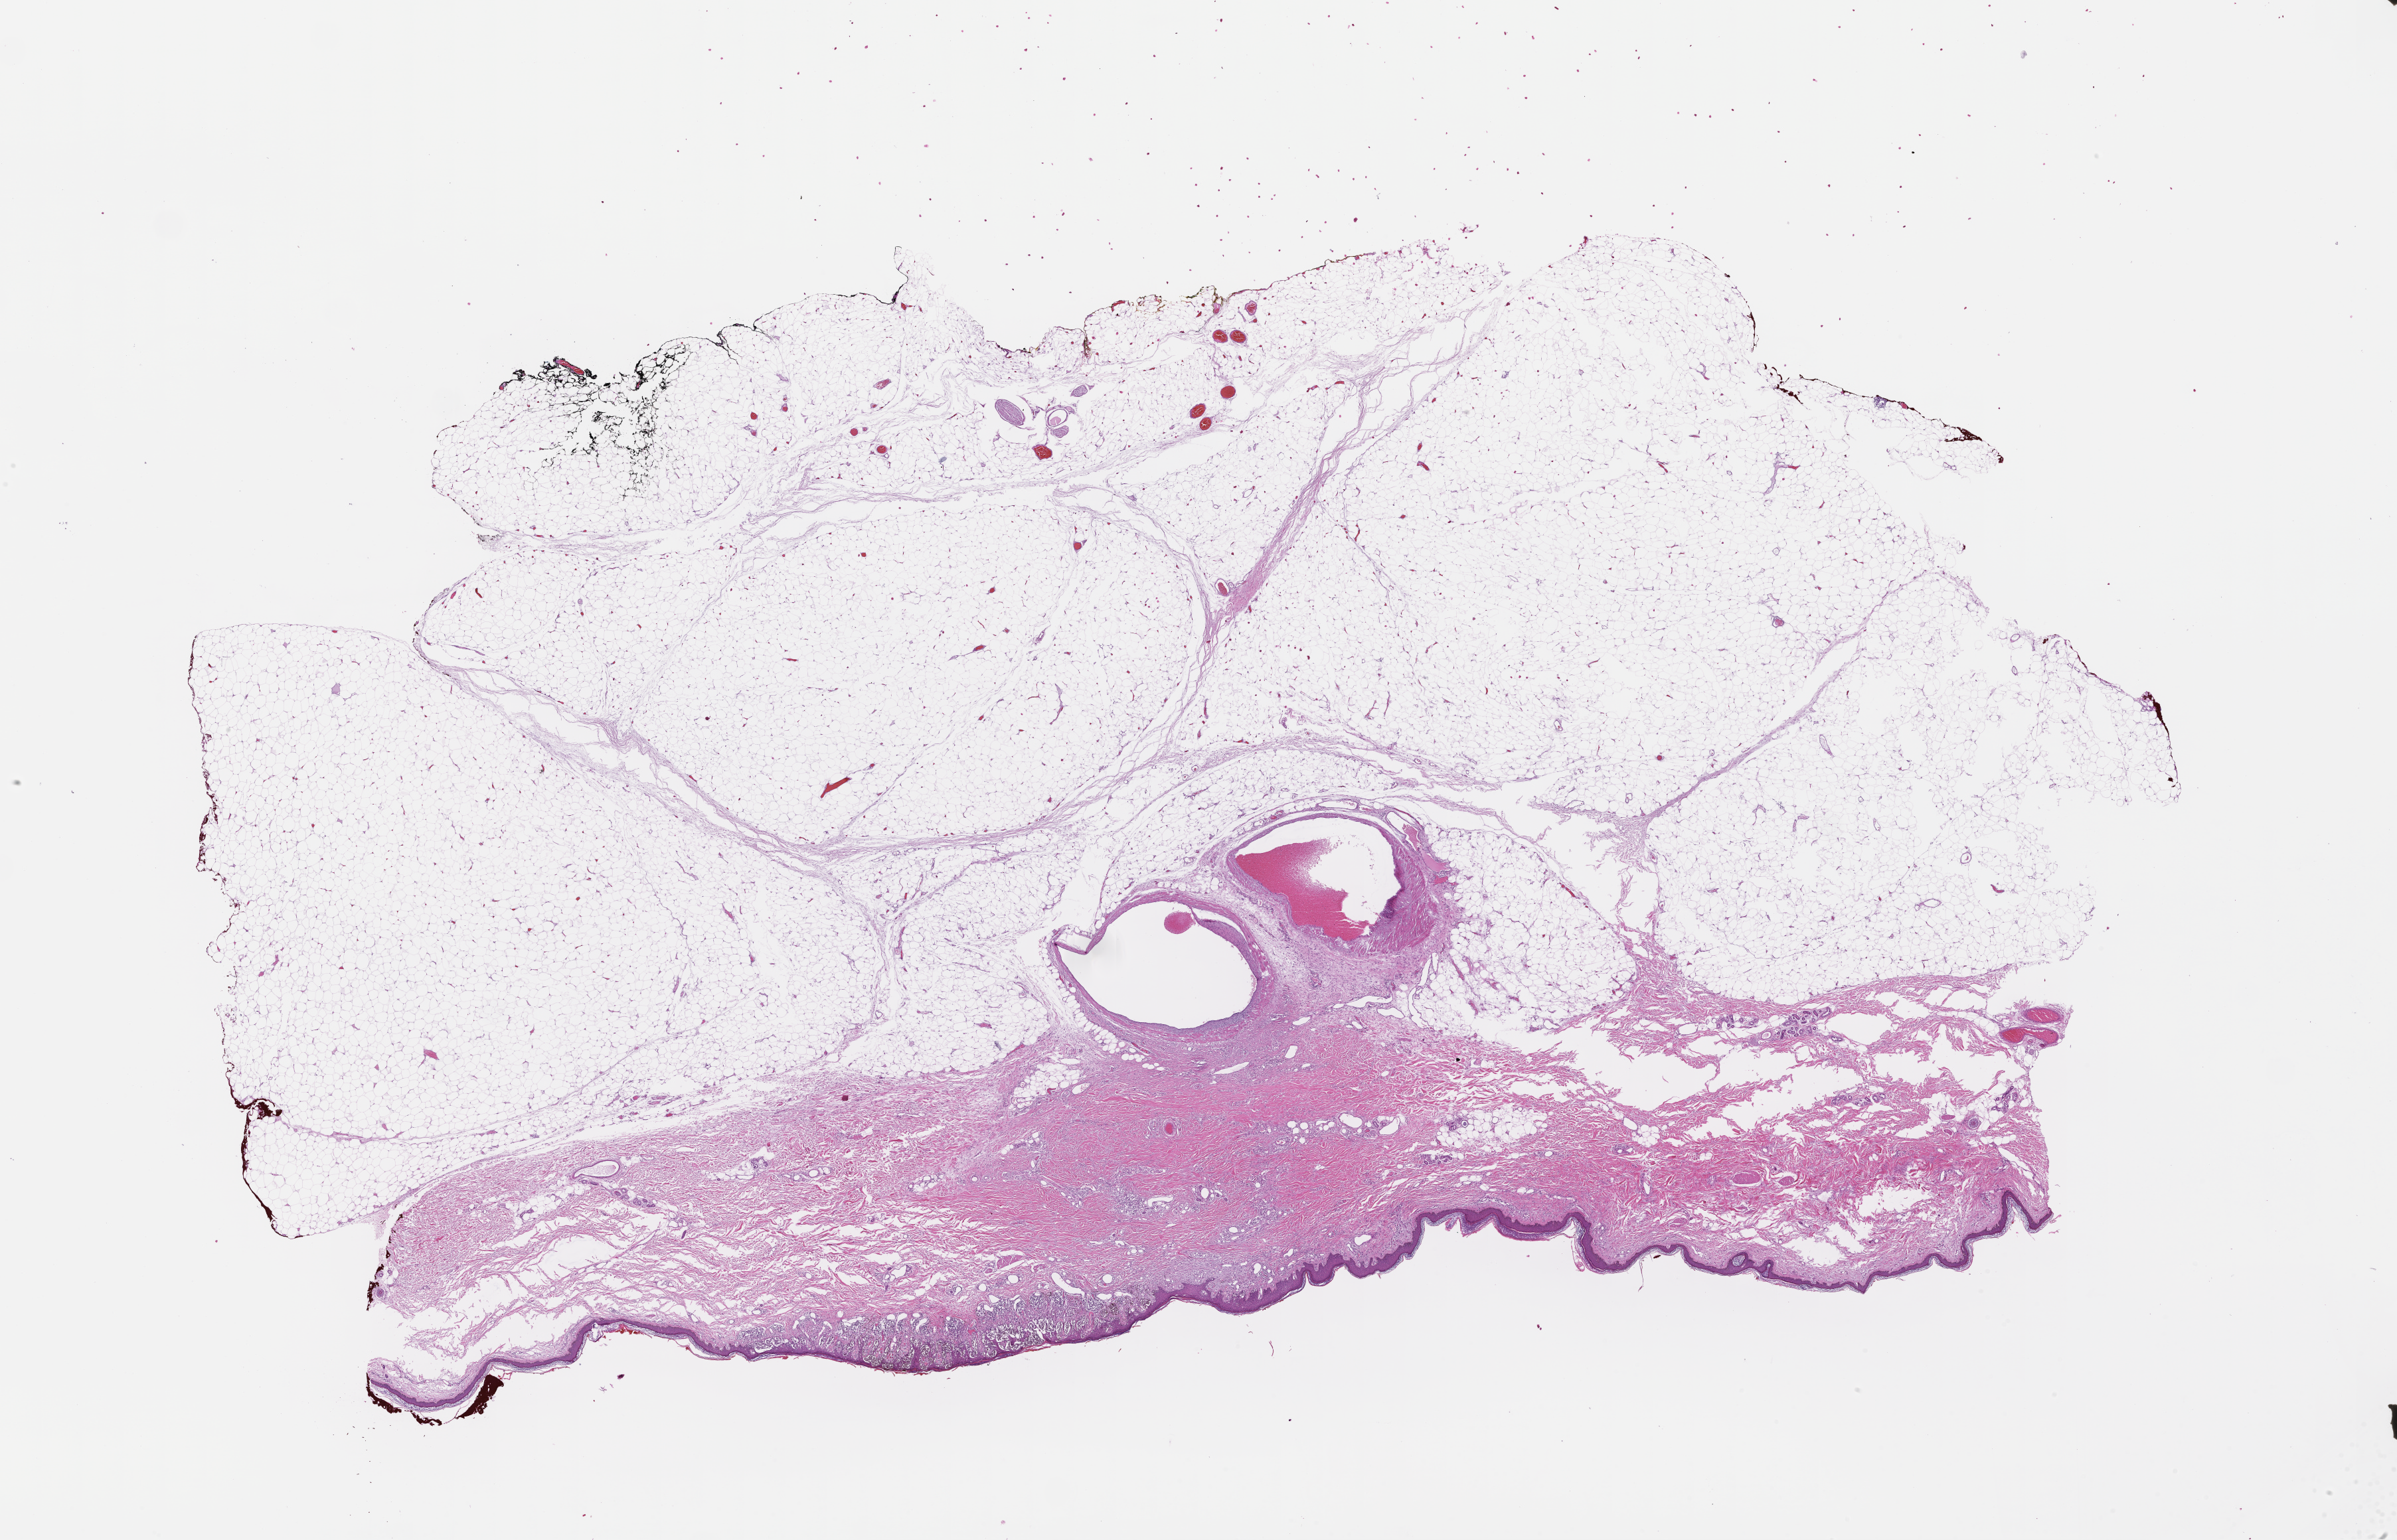
Hematoxylin and eosin (H&E) whole-slide image — shown as a low-resolution overview of the whole scanned area (about 29.1 x 18.7 mm); formalin-fixed paraffin-embedded section; tissue site: skin; specimen time point: archival tissue. Patient: female.
This section: primary tumour tissue. Diagnosis: Melanoma.